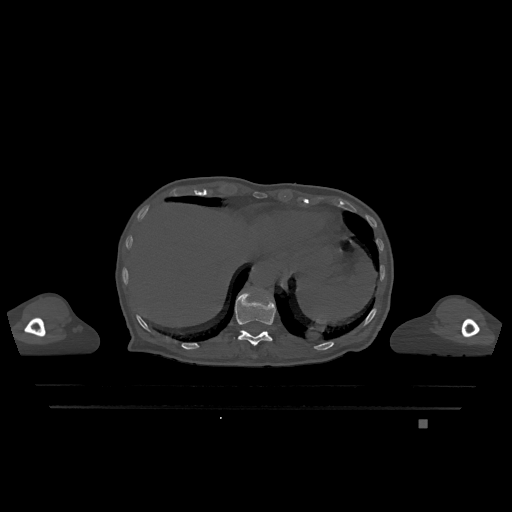
CT including the spine, one axial slice; position 584 of 1317 along the scan axis; bone window (W 1800 / L 400 HU); 0.5 mm slice thickness; 512 × 512 image matrix. Patient: female, 74 years. From the clinical record (not read from this slice): primary cancer: lung; vertebrae with lytic lesions (as recorded): T1, T4, T5, T6, L4, L5.
Structures marked on this image (semi-automatically segmented with operator editing):
- T11 vertebra: bounding box (x1, y1, x2, y2) in pixels: (235, 291, 276, 346)